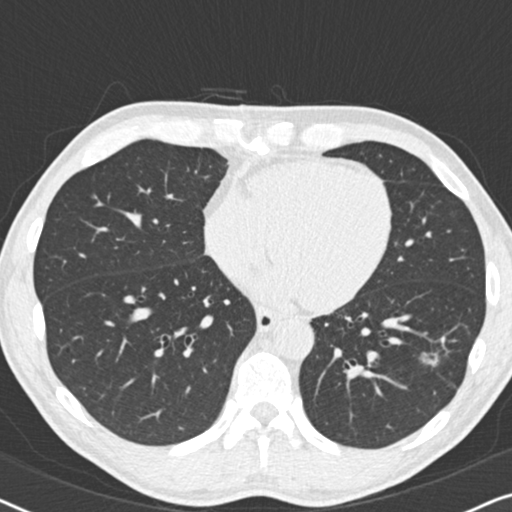
Axial slice from a low-dose chest CT screening exam, second annual screen, lung window (W 1500 / L -600 HU), 2 mm slice thickness, slice 123 of 208 in the series. Male participant, aged 59 years at enrolment. Current smoker at enrolment.
- Lesion marked by an expert reader, box from (x=413, y=338) to (x=460, y=381) px.
- The screening reader recorded 2 non-calcified nodules or masses ≥4 mm on this exam (left lower lobe, right middle lobe); which of them this box marks is not recorded.
- Official screen result: positive, other.
- Participant outcome: lung cancer diagnosed 484 days after this screen (after the third annual screen) — adenocarcinoma, NOS, left lower lobe, poorly differentiated (G3), stage IA (AJCC 6th edition), 20 mm at pathology.